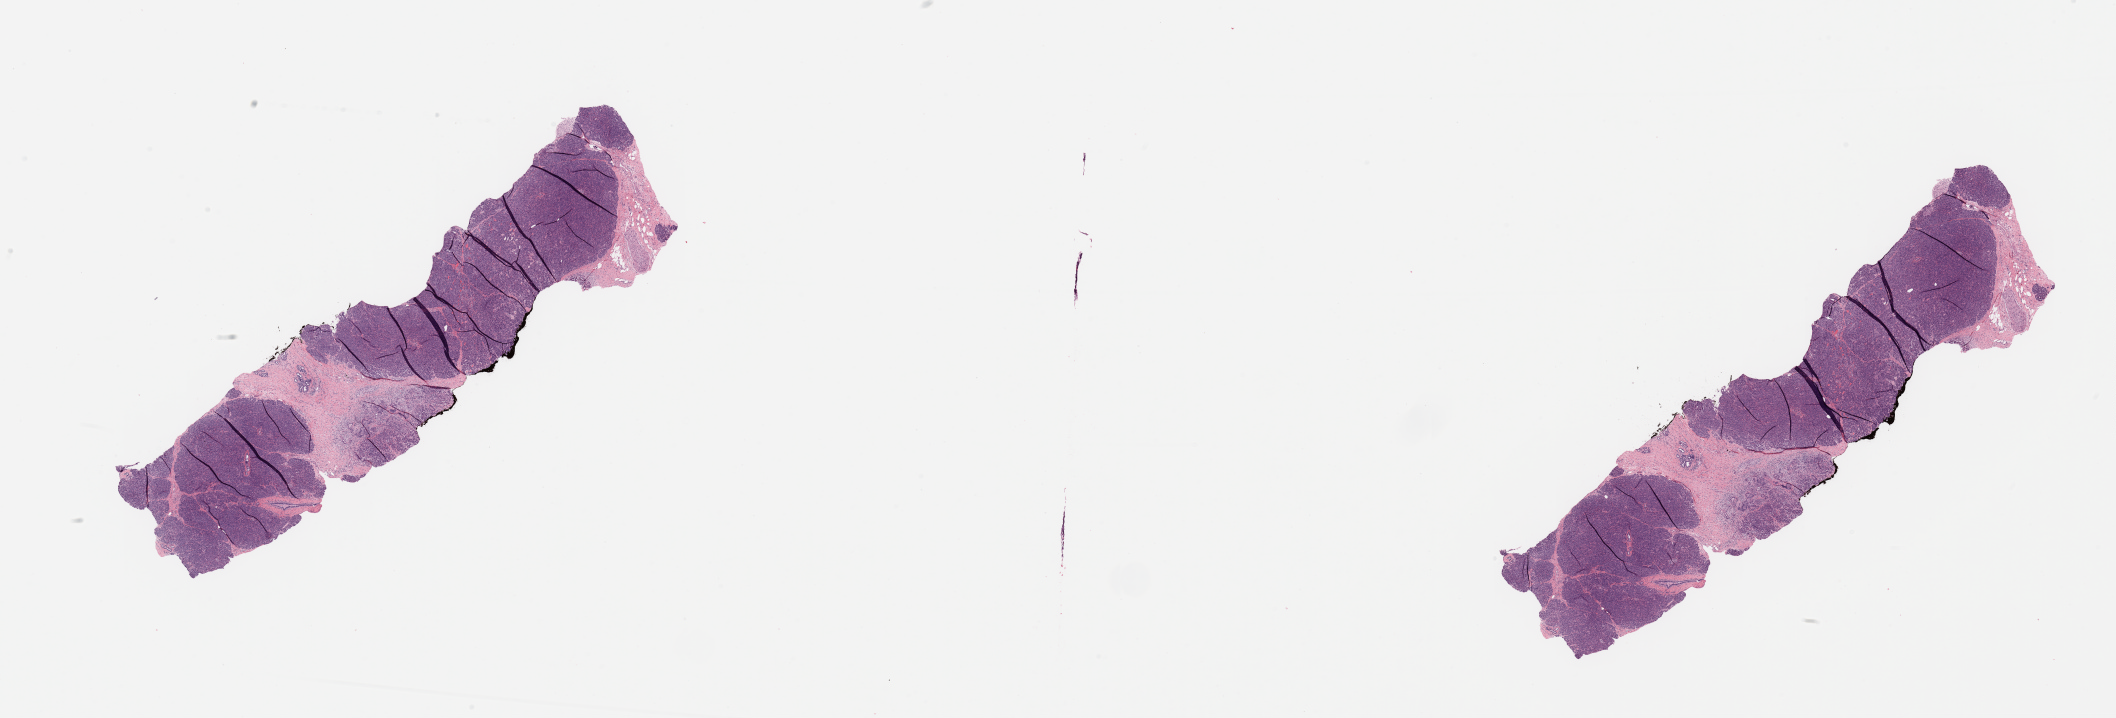
Whole-slide histology image, H&E — low-resolution overview of the scanned area, about 33.5 x 11.4 mm (from a 20x scan); normal (non-tumour) tissue sample, sampled site: pancreas. 67-year-old male patient.
- this section: normal (non-tumour) tissue from the same patient
- patient diagnosis: Infiltrating duct carcinoma, NOS